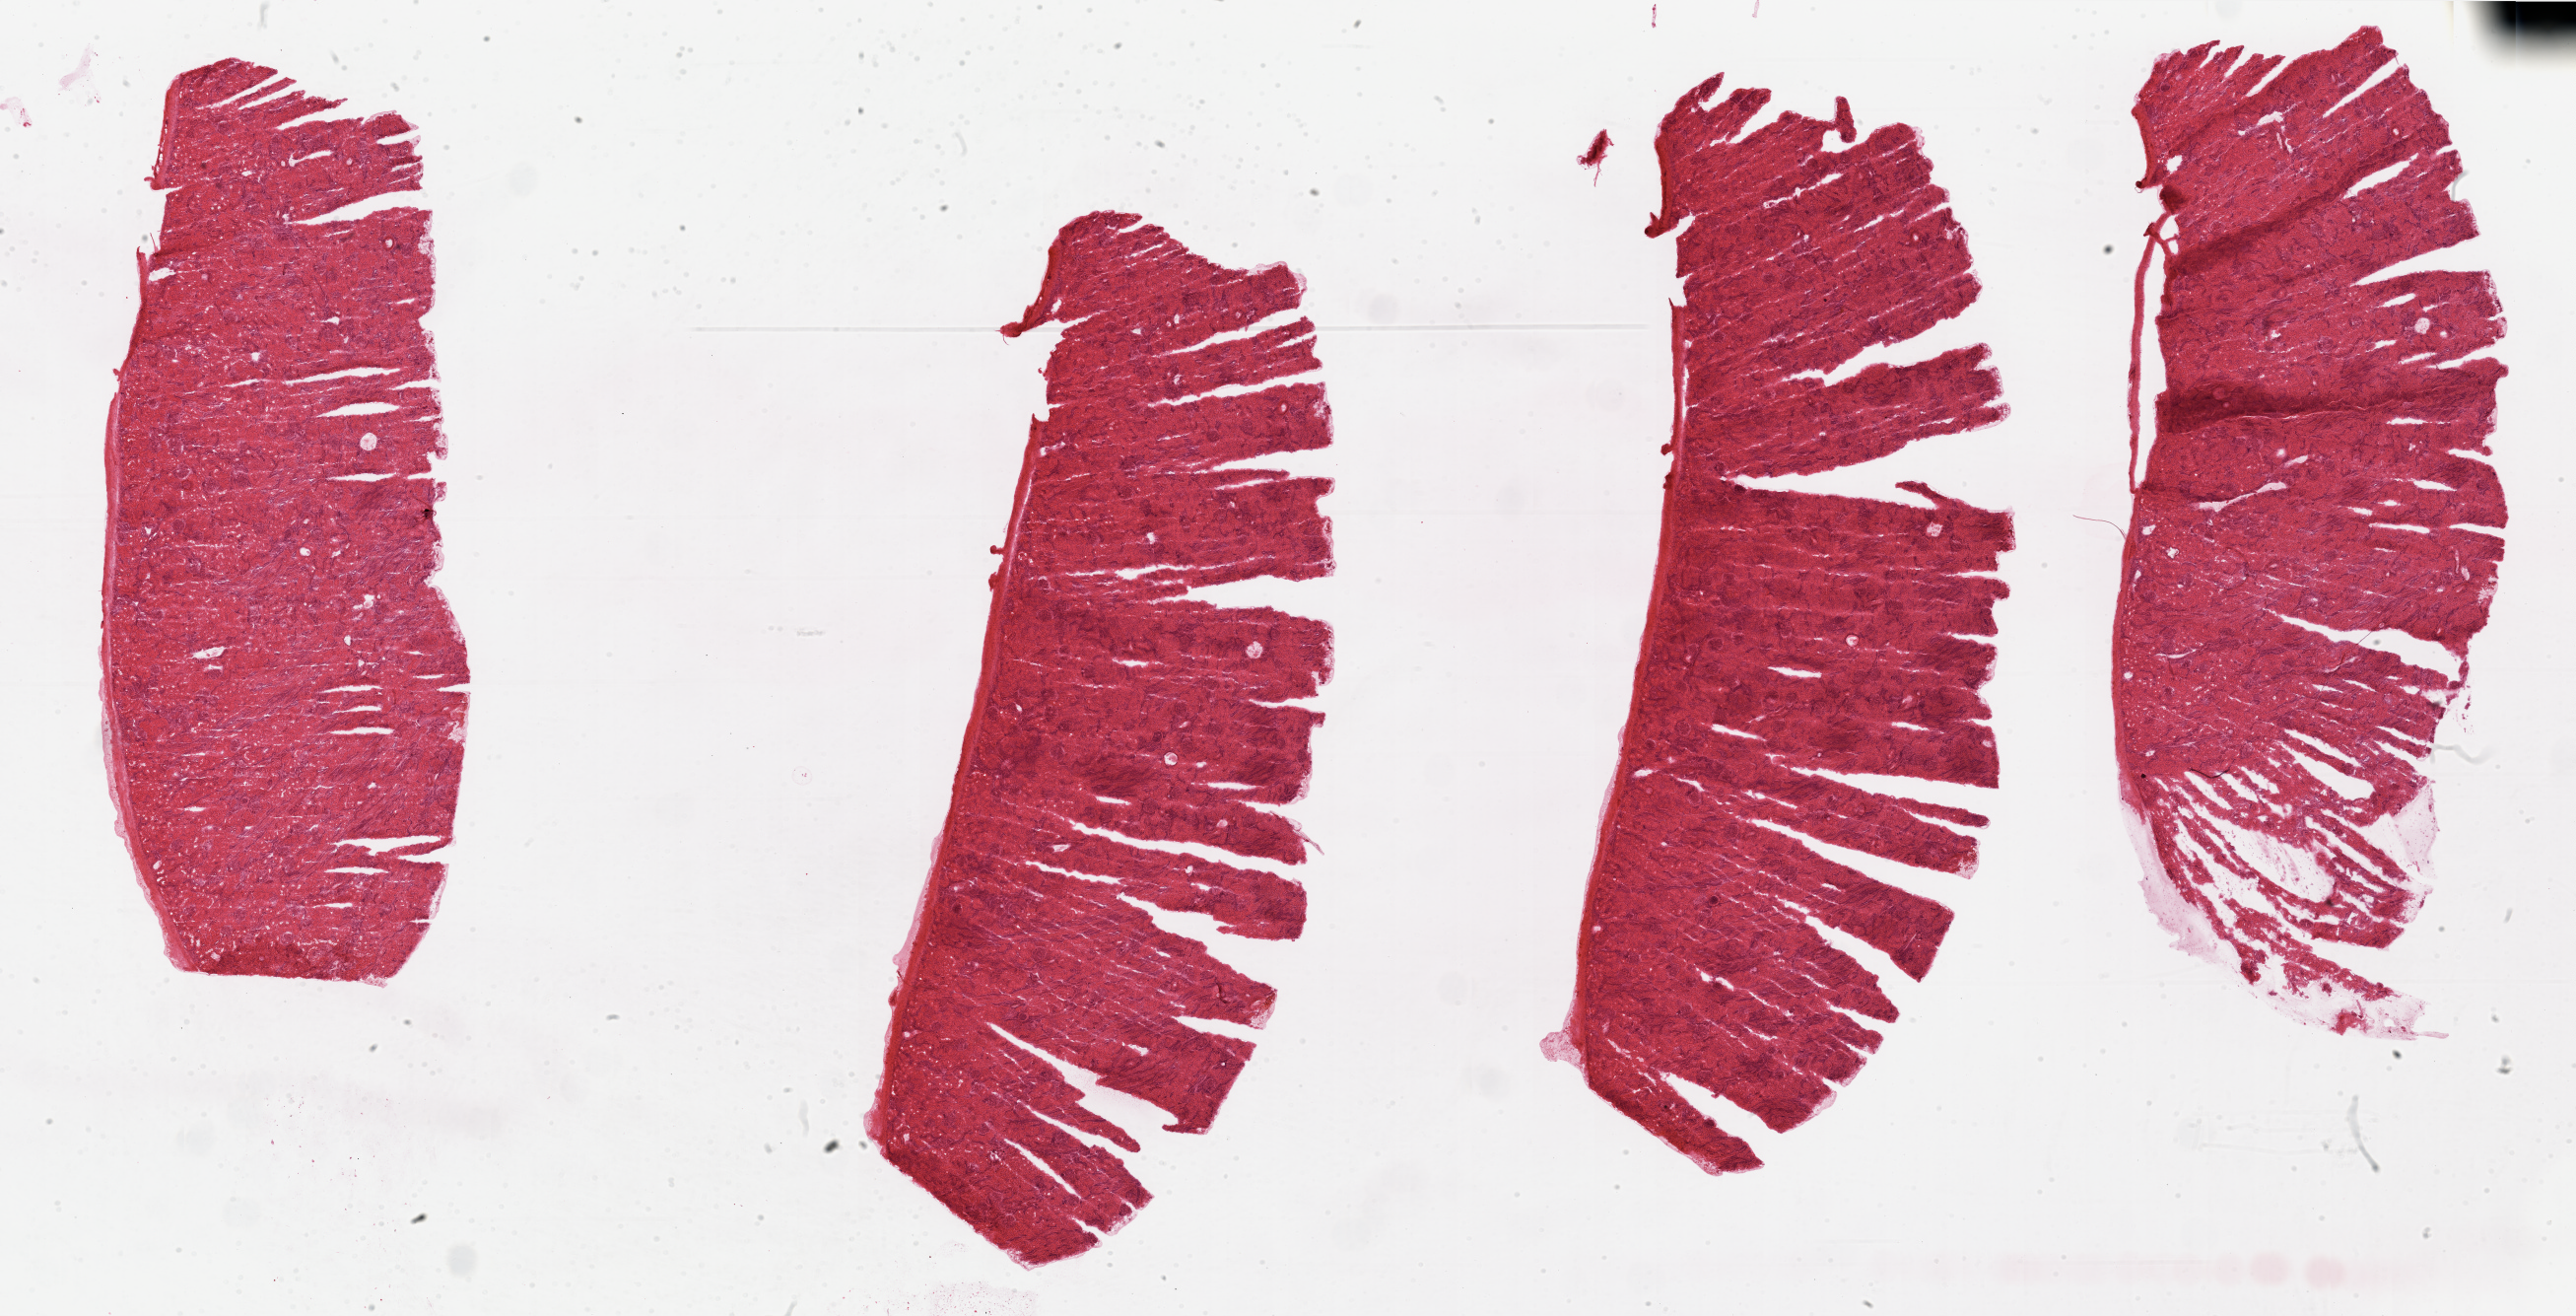
Whole-slide histology image, H&E-stained, shown as a low-resolution overview of the whole scanned area (about 41.3 x 21.1 mm, from a 20x scan), normal (non-tumour) tissue sample, sampled site: kidney. Patient: female, age 49 years.
- this section: normal (non-tumour) tissue from the same patient
- patient diagnosis: Renal cell carcinoma, NOS